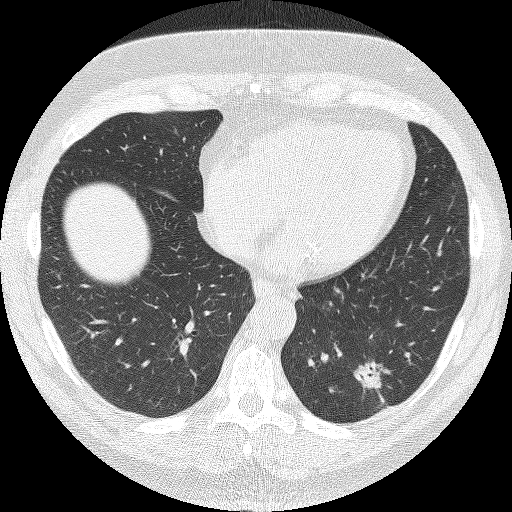
Chest CT (low-dose screening protocol), one axial image. First (baseline) screen. Lung window (W 1500 / L -600 HU). 2 mm slice thickness. Lung (sharp) reconstruction kernel (FC51). 120 kVp. 512 × 512 image matrix, field of view 349 × 349 mm. Male, age 62 years at enrolment. Current smoker at enrolment.
- Expert reader's lesion annotation, bounding box (x1, y1, x2, y2) in pixels: (348, 353, 405, 404).
- The screening reader recorded 2 non-calcified nodules or masses ≥4 mm on this exam; which of them this box marks is not recorded.
- Official screen result: positive, change unspecified: nodule(s) >= 4 mm or enlarging nodule(s), mass(es), or other non-specific abnormalities suspicious for lung cancer.
- Participant outcome: lung cancer diagnosed 90 days after this screen — adenocarcinoma, NOS, left lower lobe, moderately differentiated (G2), stage IA (AJCC 6th edition), 30 mm at pathology.